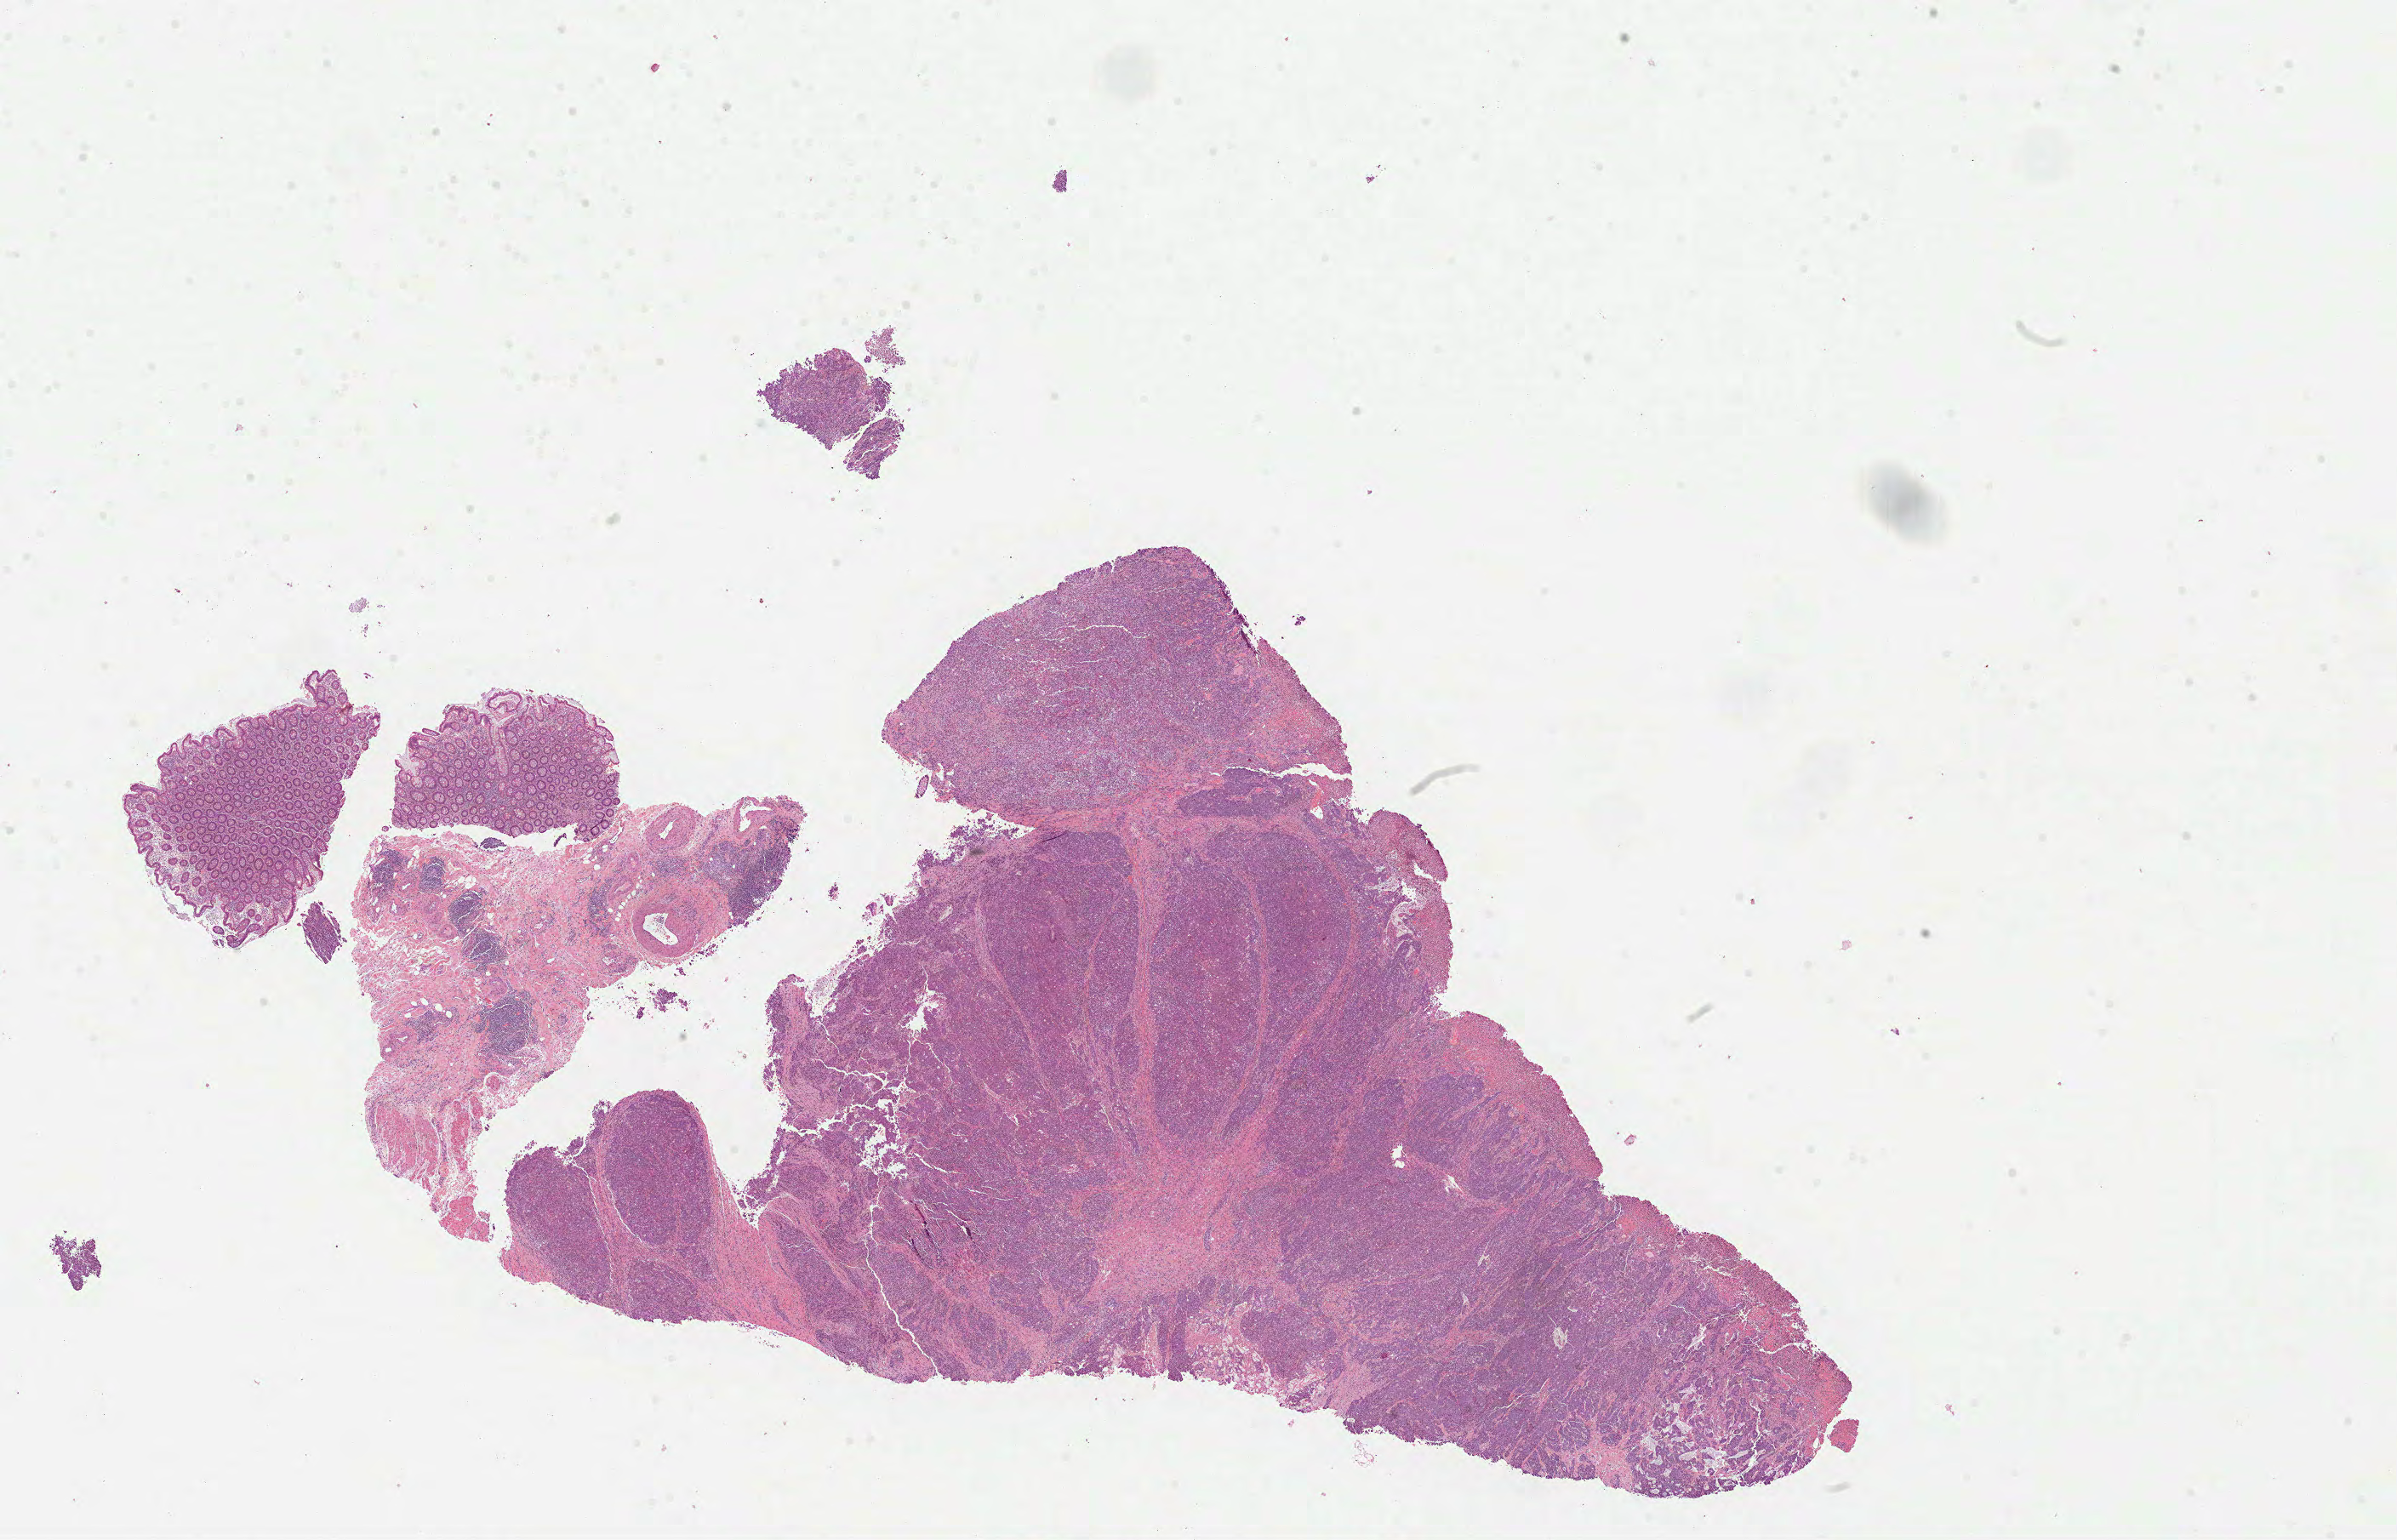
H&E whole-slide image — shown as a low-resolution overview of the whole scanned area (about 22.7 x 14.6 mm), formalin-fixed paraffin-embedded (FFPE) diagnostic section, colon, primary tumour sample. Patient: male, age at initial diagnosis 58 years.
• pathologic diagnosis: Adenocarcinoma, NOS (ascending colon)